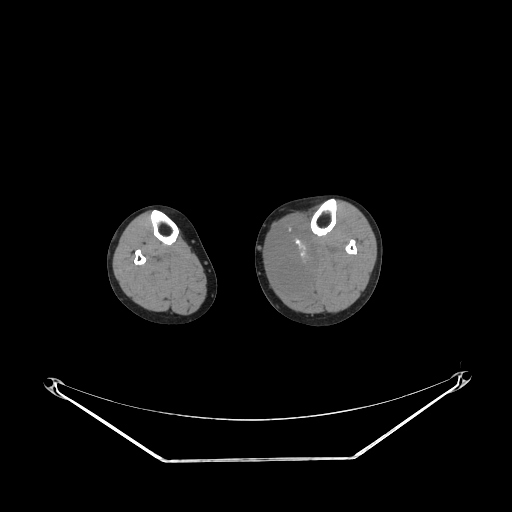
CT of an extremity soft-tissue mass (from a PET/CT study), one axial slice; slice 137 of 223 in the series (ordered by position); reconstruction kernel STANDARD; soft-tissue window (W 400 / L 40 HU); 512 × 512 image matrix, field of view 500 × 500 mm. Female patient. From the clinical record (not read from this slice): histological type: extraskeletal high grade osteogenic sarcoma; grade: high; site of the primary tumour: left calf.
Outlined on this slice (expert contour drawn on MRI and transferred to this co-registered scan by the dataset authors):
- gross tumour volume (mass): box from (x=270, y=228) to (x=314, y=286) px